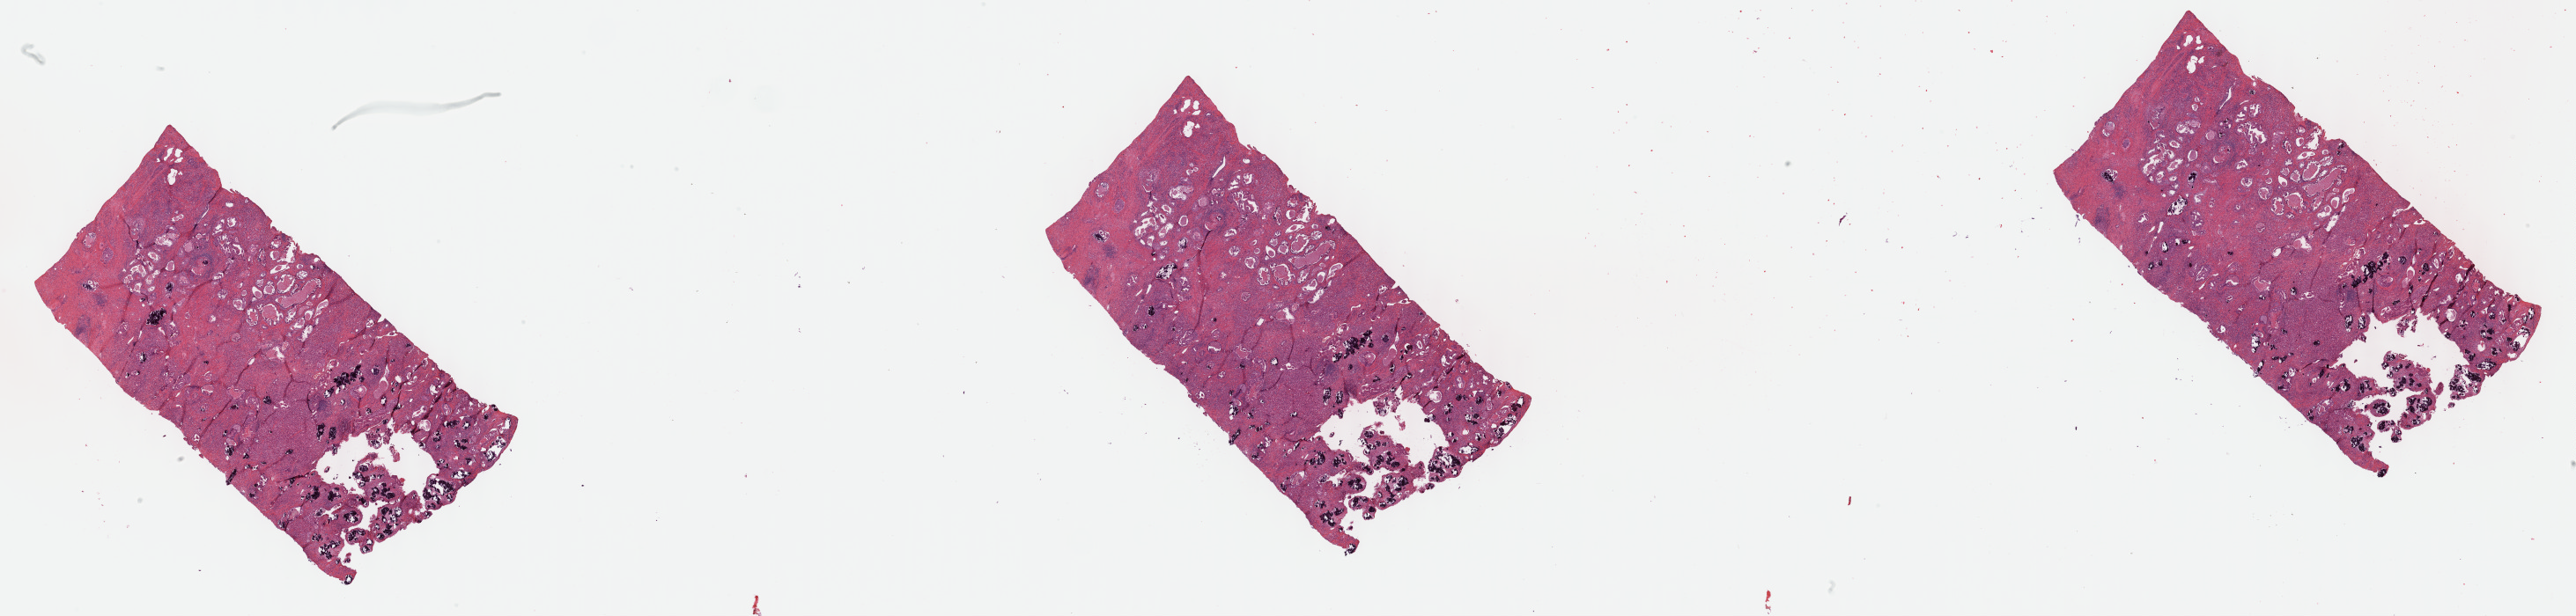
Whole-slide histology image, H&E-stained, a low-resolution overview of the entire scanned area, about 47.3 x 11.3 mm, FFPE section, primary tumour sample from the prostate. Male patient; age at initial diagnosis 63 years. Gleason score: 10 (5+5).
Pathologic diagnosis: Adenocarcinoma, NOS.